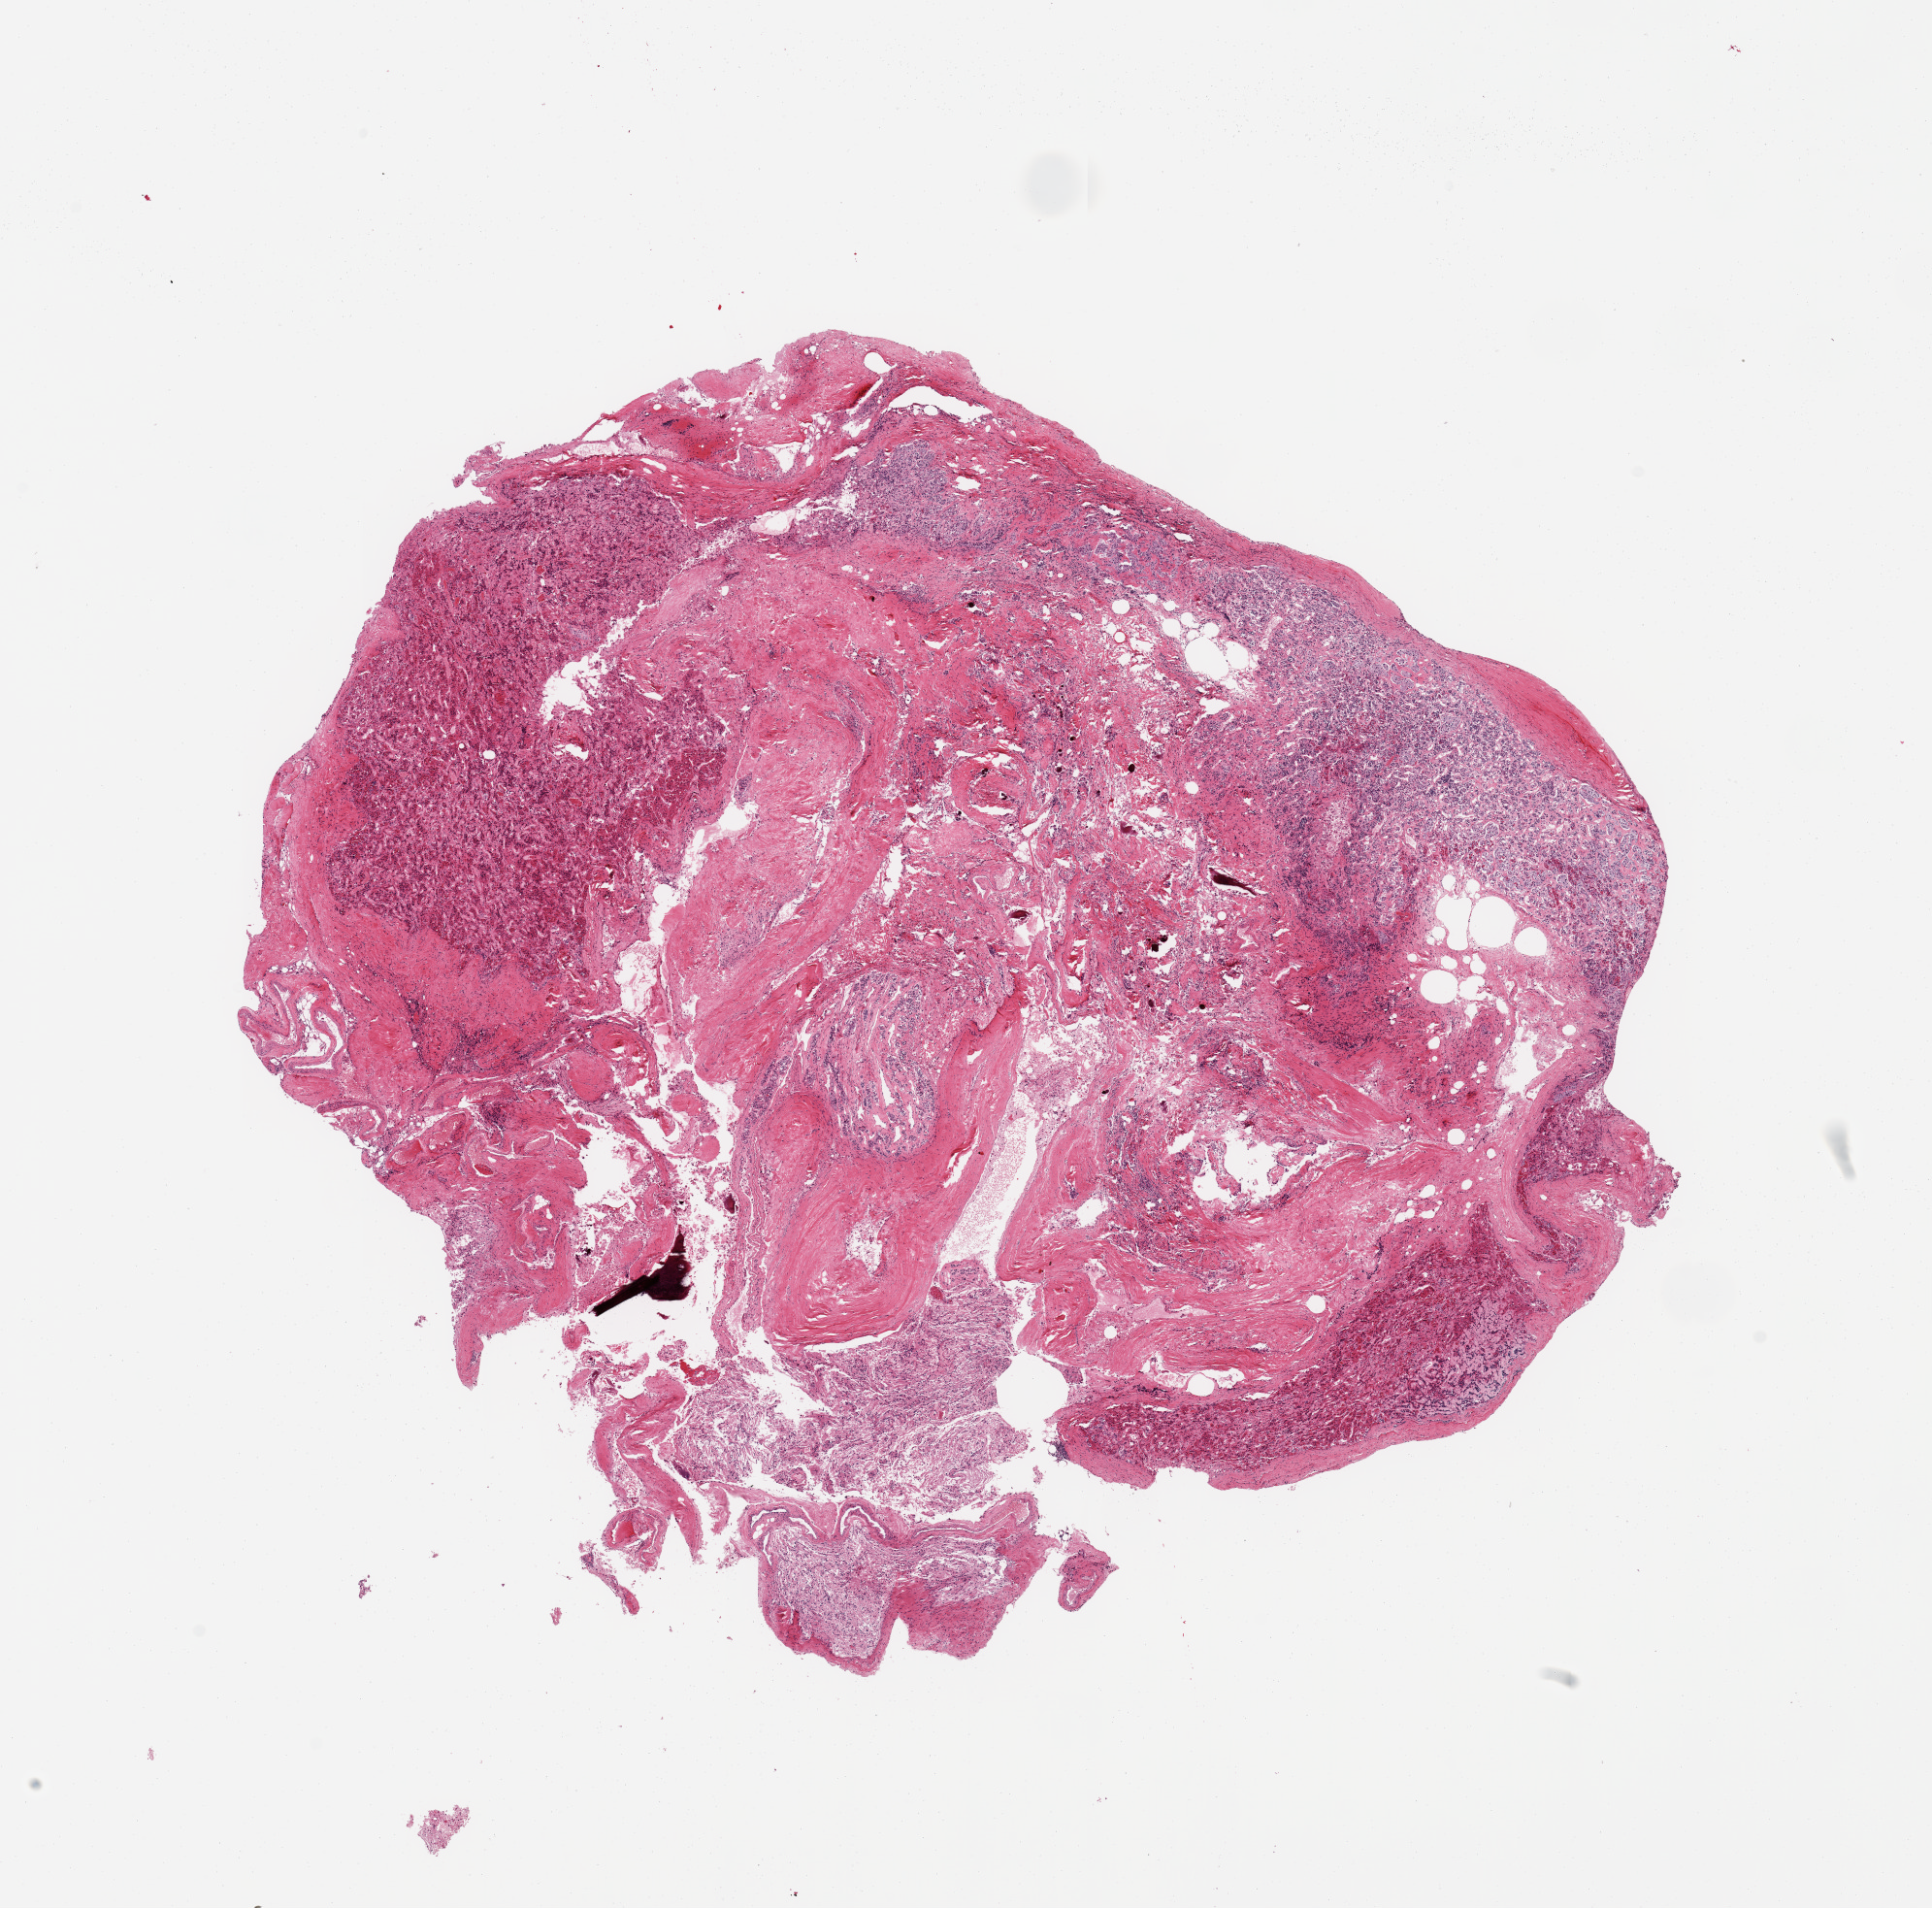
Whole-slide image, haematoxylin and eosin stain — whole scanned area (about 15.8 x 15.6 mm, slide scanned at 20x) shown as a low-resolution overview, PAXgene-fixed, paraffin-embedded tissue, section of pituitary (target tissue), donor tissue sample. Donor: male.
Pathologist's review note for this sample: 1 piece; outer rim of adeno- & neurohypophysis with large central stromal core.